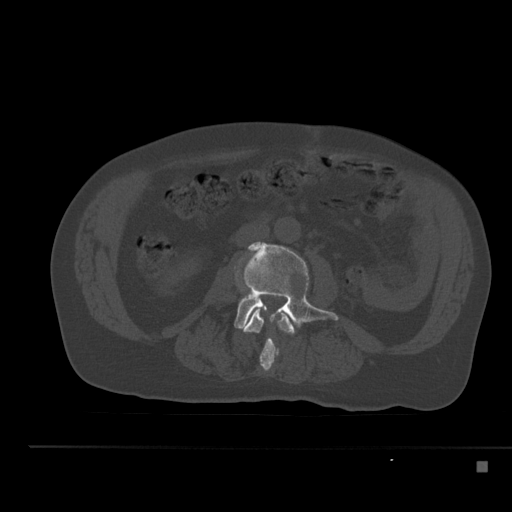
CT including the spine, one axial slice. Position 170 of 517 along the scan axis. Reconstruction kernel Br40s. 120 kVp. Bone window (W 1800 / L 400 HU). 1.5 mm slice thickness. 512 × 512 image matrix, field of view 408 × 408 mm. Patient: male, 70 years. Case-level facts recorded for this patient, not image findings: primary cancer: renal.
Outlined on this slice (semi-automatically segmented with operator editing):
- L2 vertebra: bounding box [x1, y1, x2, y2] px = [241, 310, 295, 372]
- L3 vertebra: [234, 240, 339, 329]